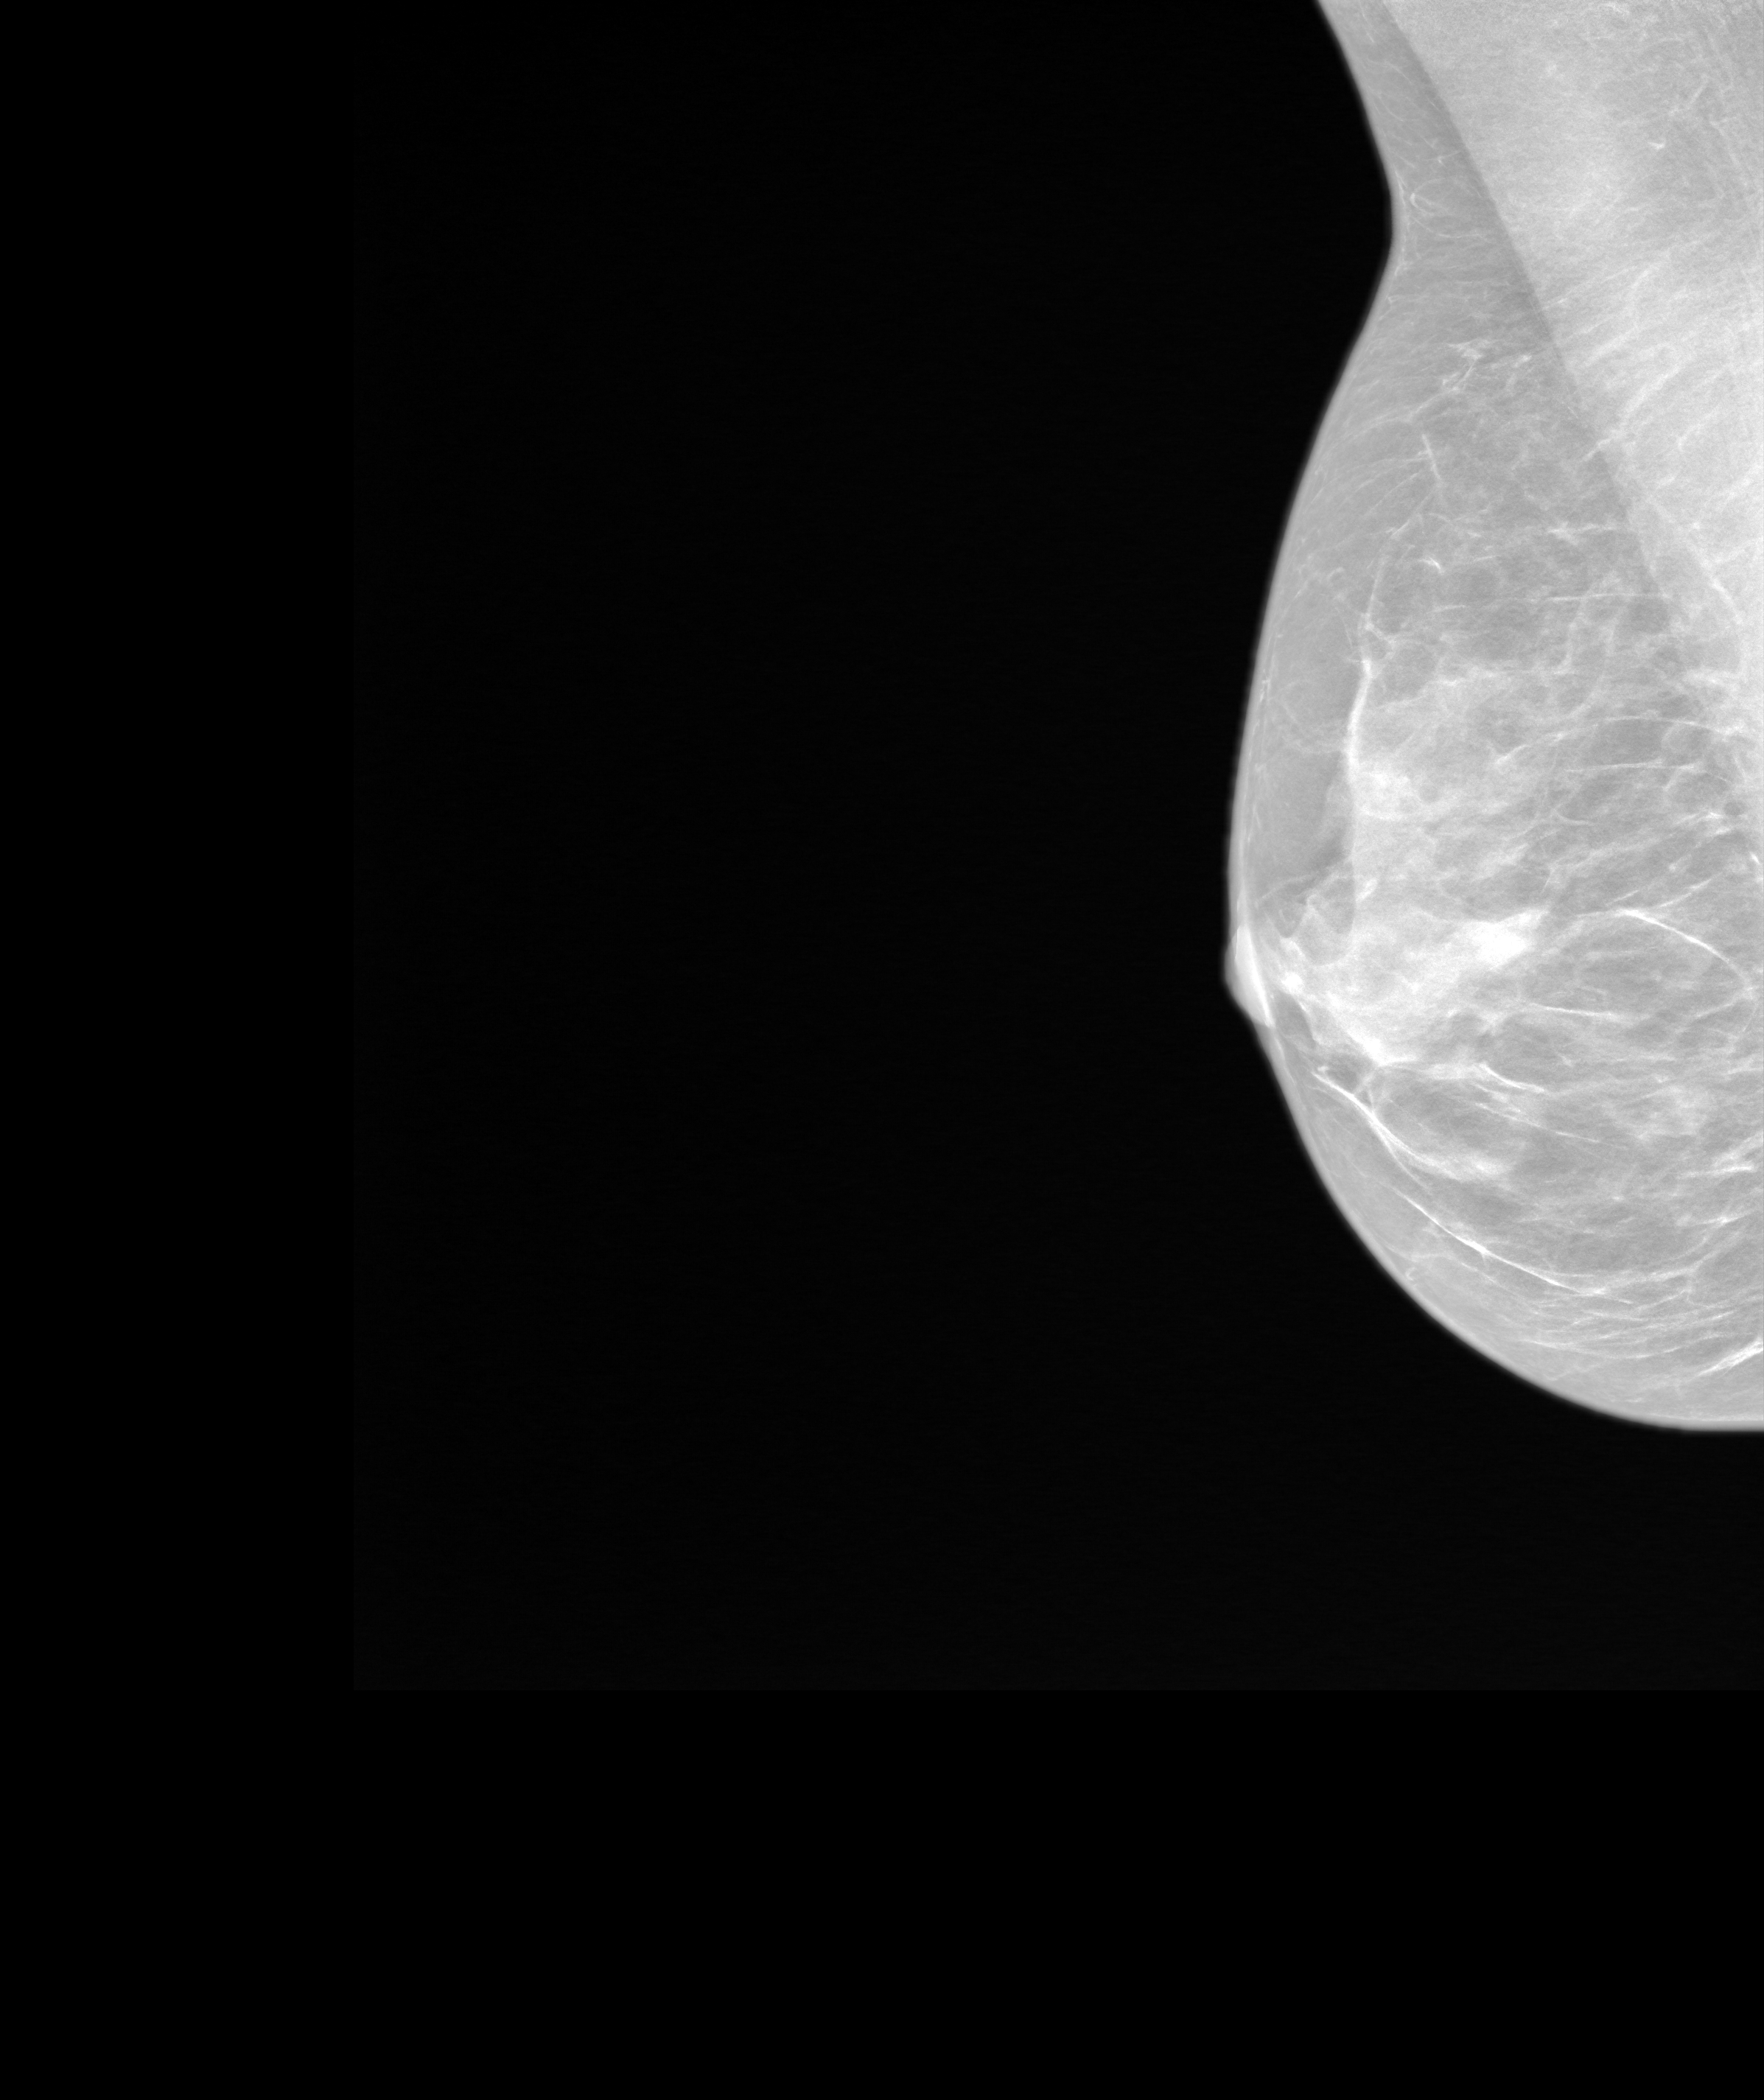
Screening examination. Patient: female, 66 years.
Image type: synthesized 2-D view from tomosynthesis. Breast: right. Projection: MLO view.